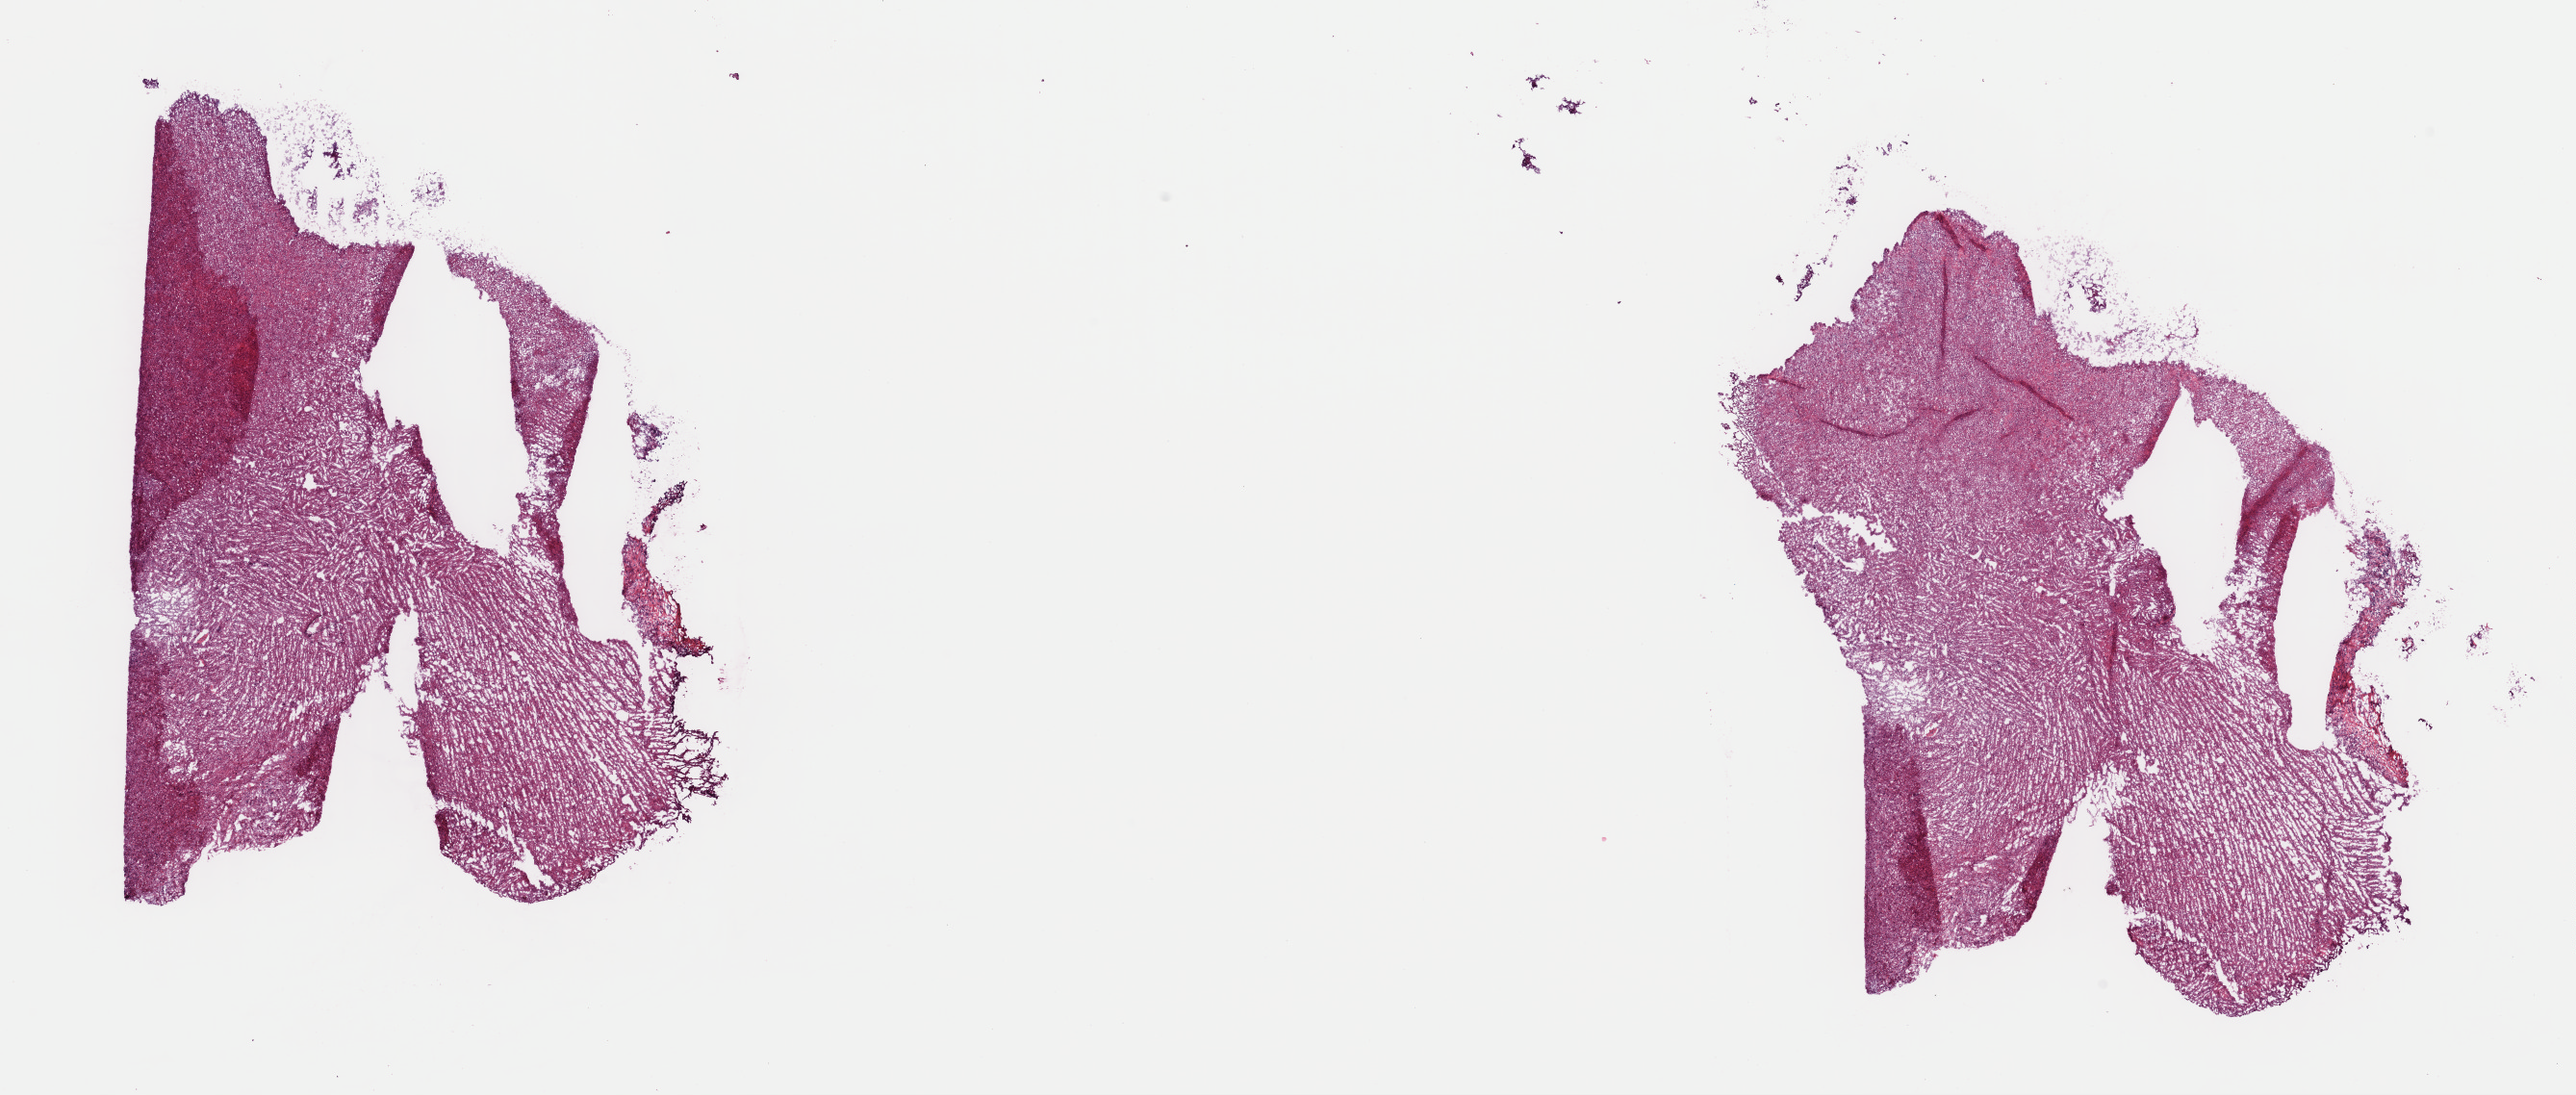
Digitized Hematoxylin and eosin (H&E) stained tissue section (whole slide), whole scanned area (about 21.1 x 9.0 mm) shown as a low-resolution overview, frozen section from the top of the tissue portion, sample: recurrent tumour, brain. Patient: female, age at initial diagnosis 43 years. Pathologist review of this section (percent, as recorded): tumour cells 20%, tumour nuclei 70%, normal cells 20%, stromal cells 60%, necrosis 0%. Inflammatory infiltration, as recorded: lymphocyte infiltration 0%, monocyte infiltration 0%, neutrophil infiltration 0%.
* this section: recurrent tumour
* patient diagnosis: Mixed glioma